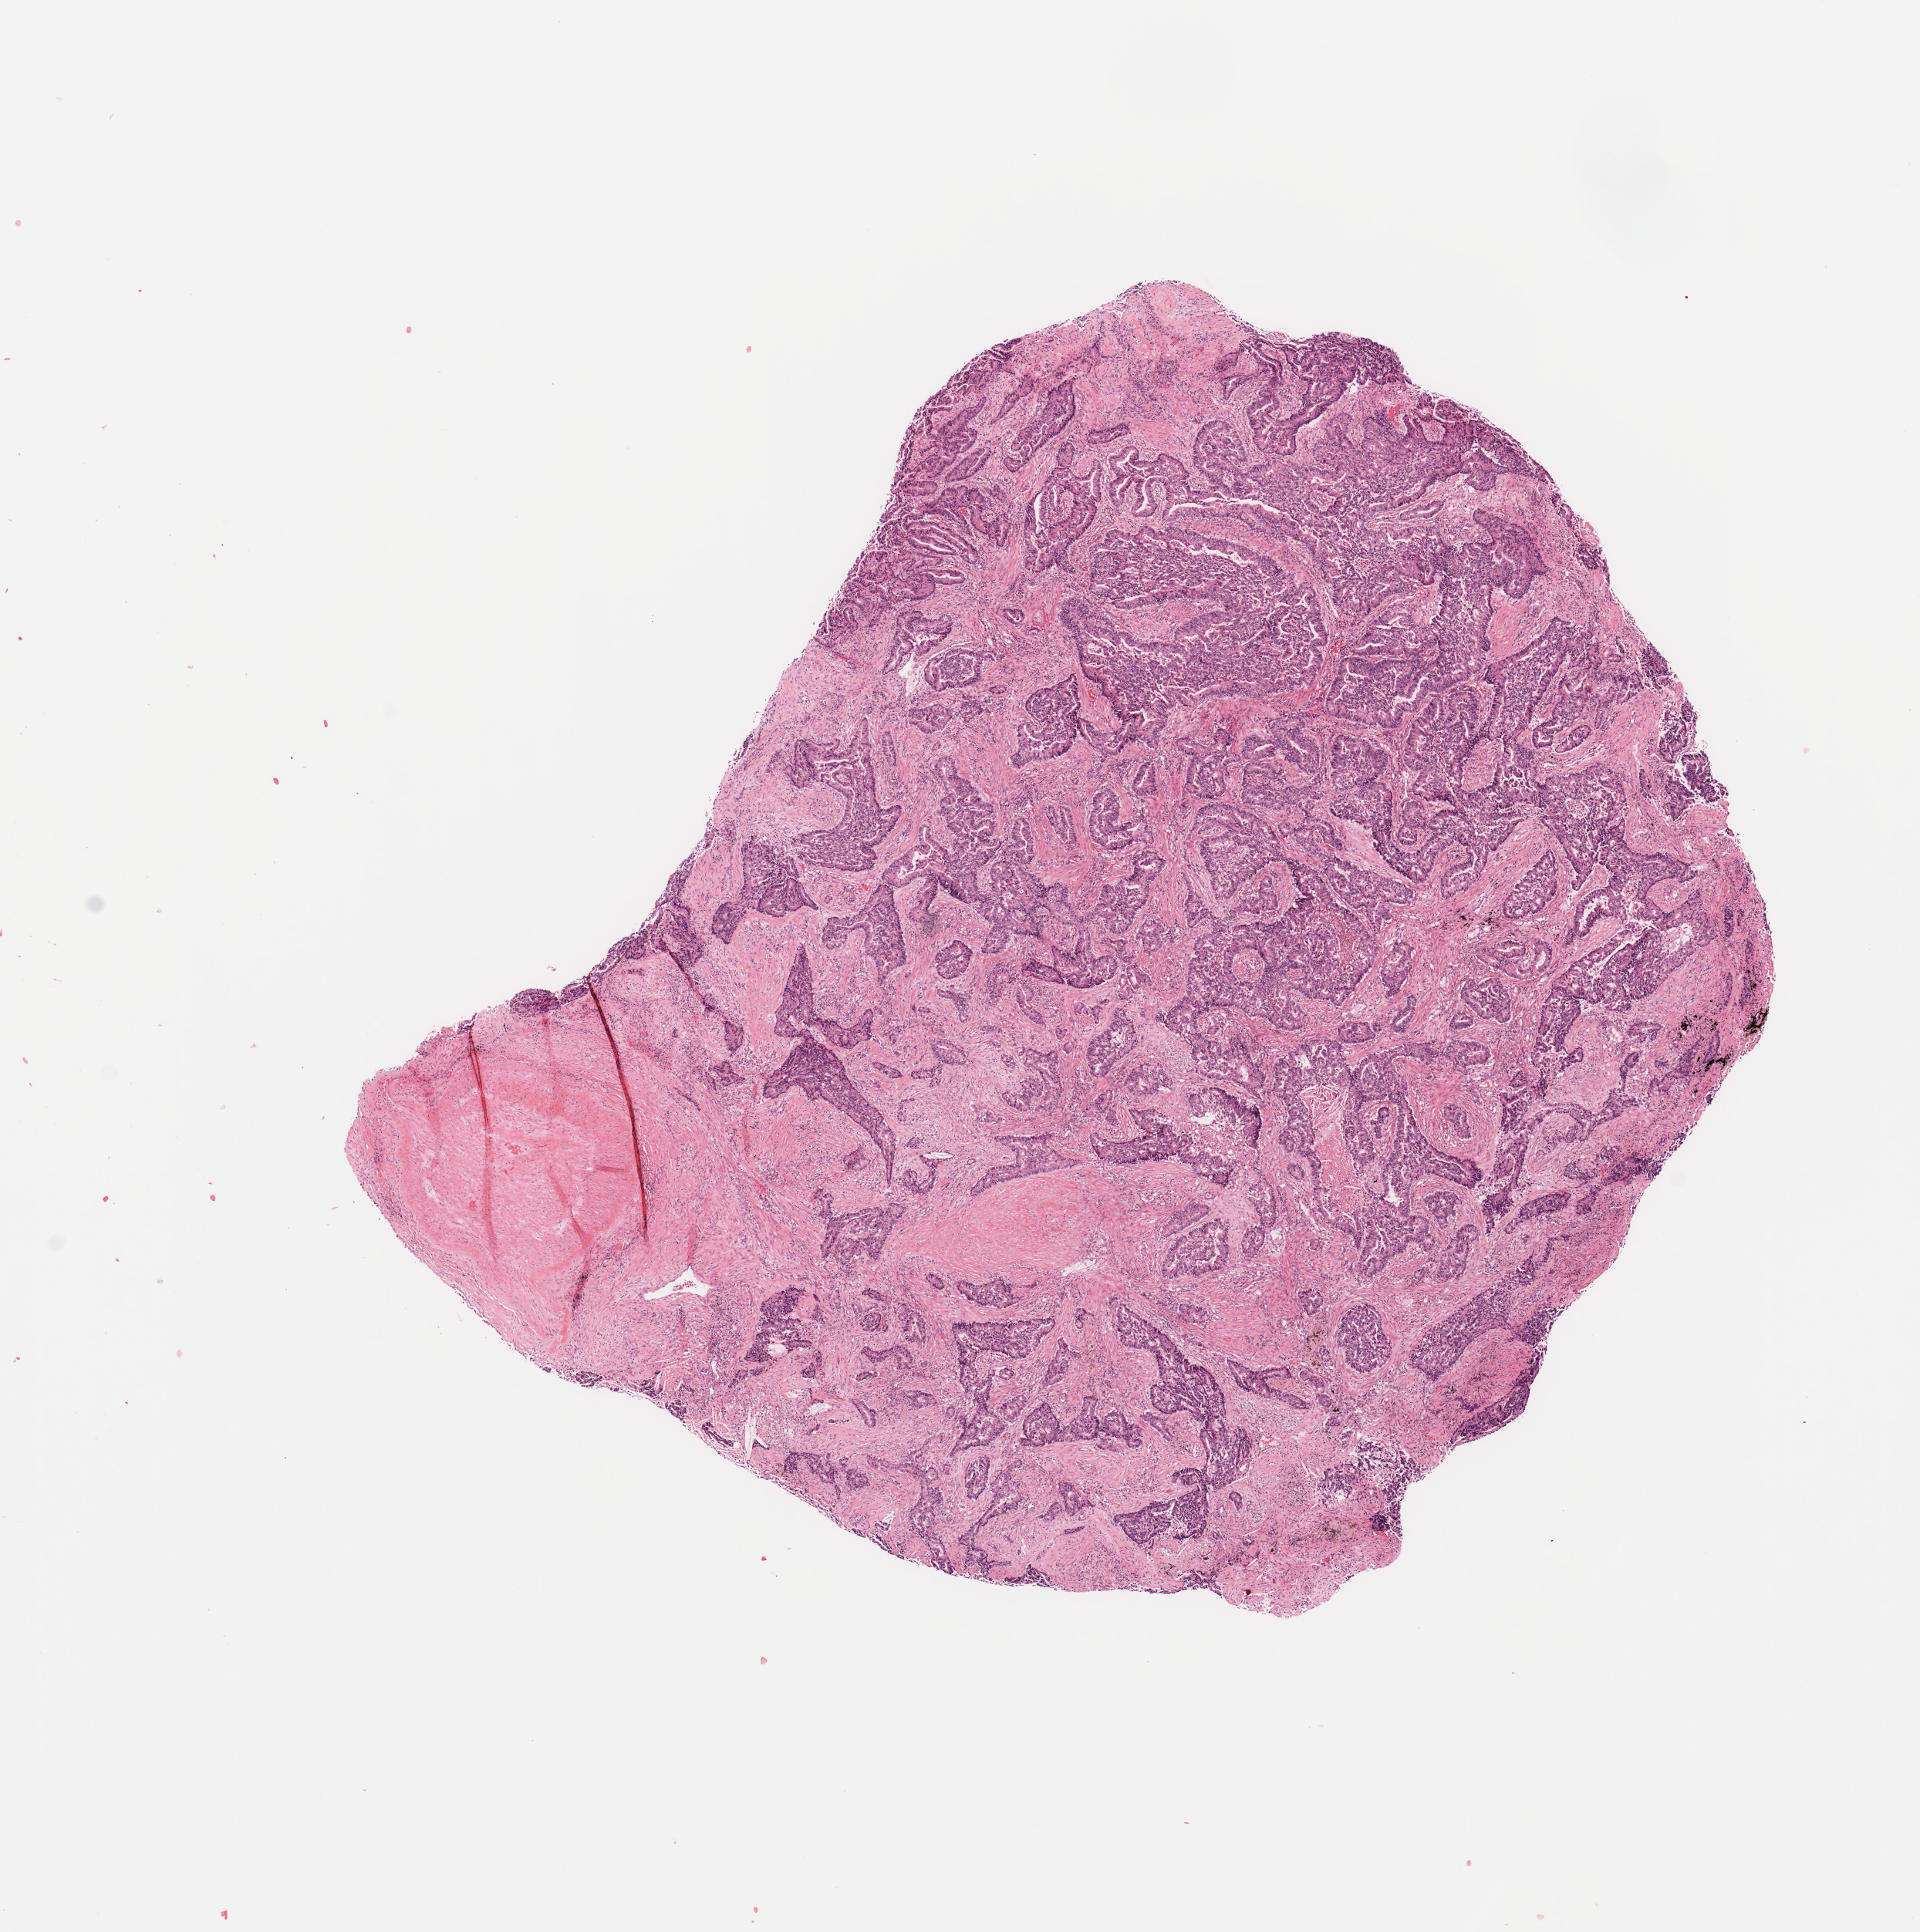
Whole-slide histology image, H&E-stained — whole scanned area (about 9.8 x 9.9 mm) shown as a low-resolution overview, tumour tissue sample, sampled site: lung. Female, 59 y/o.
Diagnosis: Adenocarcinoma, NOS.